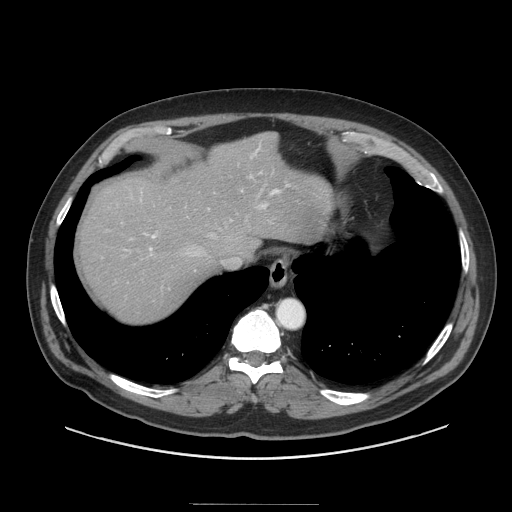
Contrast-enhanced abdominal CT (liver protocol), one axial slice. Reconstruction kernel STANDARD. 140 kVp. Soft-tissue window (W 400 / L 40 HU). 512 × 512 image matrix, field of view 440 × 440 mm. Case-level facts recorded for this patient, not image findings: diagnosis: hepatocellular carcinoma (patient treated with transarterial chemoembolisation; whether this scan precedes or follows treatment is not stated here); TNM stage (as recorded): Stage-I; Child-Pugh class: A; tumour size: 4 cm.
Annotated regions visible in this slice (semi-automatic segmentation, software-assisted and operator-edited):
- abdominal aorta: bounding box <278,300,303,327> (left, top, right, bottom; pixels)
- liver parenchyma outside the tumour (the mass and vessels are separate outlines, so this box may not span the whole liver): <78,132,332,320>
- liver vessels: <145,149,280,256>